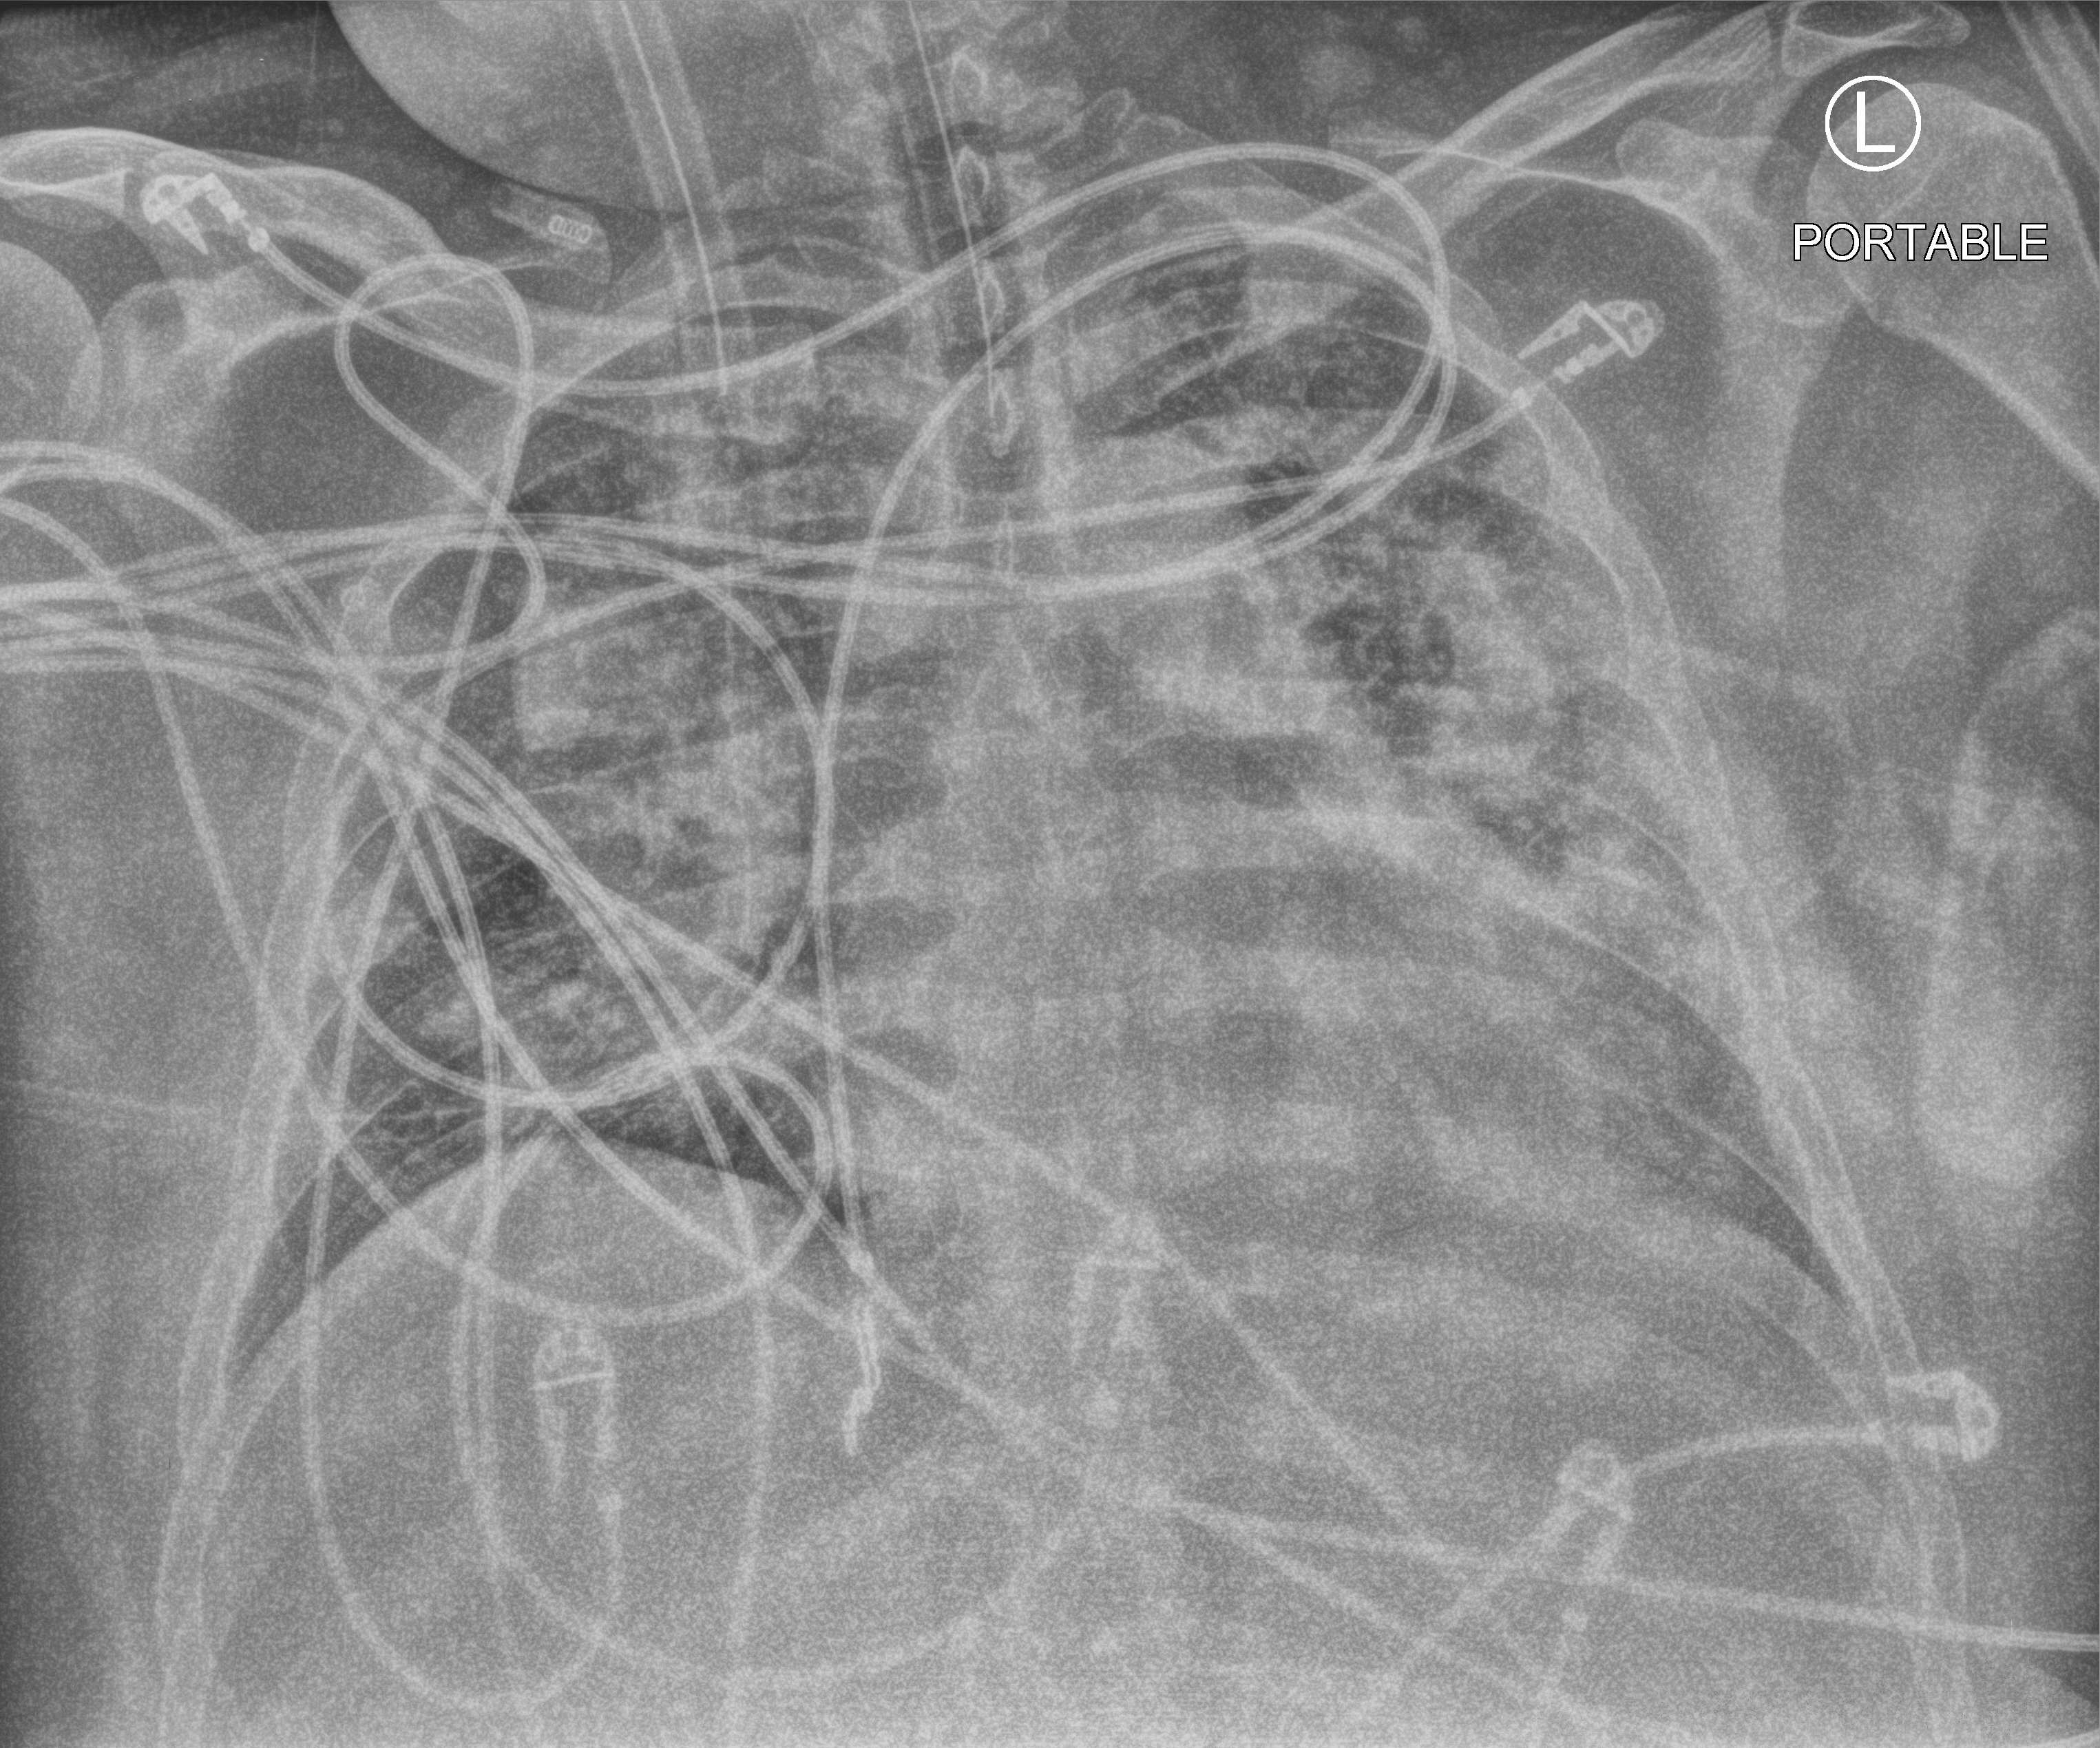
Chest X-ray (portable); anteroposterior (AP) projection. Adult patient hospitalised with COVID-19, age 18–59 years.
Hospital-stay facts (about this admission, not read from this image; timing relative to this image not recorded): smoking status (admission record): former.